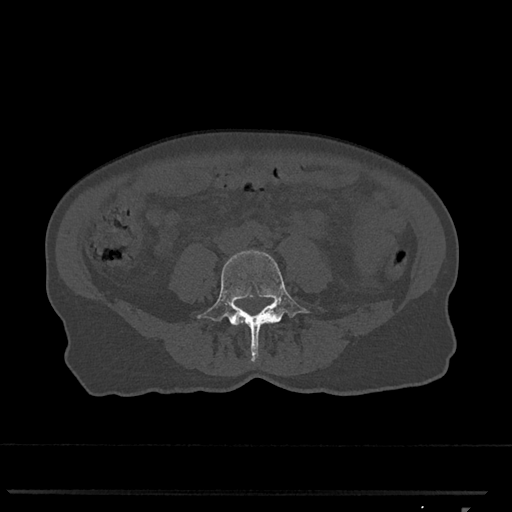
CT including the spine, one axial slice; slice 214 of 793 in the series (ordered by position); reconstruction kernel Br40s/3; bone window (W 1800 / L 400 HU); 0.5 mm slice thickness; 512 × 512 image matrix, field of view 380 × 380 mm. Patient: female, 62 years. Case-level facts recorded for this patient, not image findings: primary cancer: renal.
Structures marked on this image (semi-automatically segmented with operator editing):
- L4 vertebra: box from (x=197, y=250) to (x=310, y=362) px